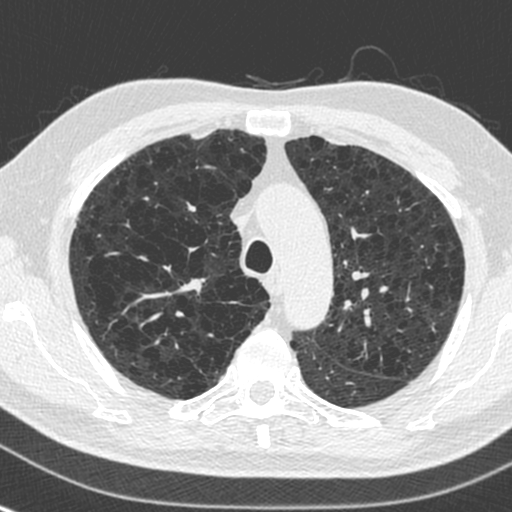
Axial slice from a low-dose chest CT screening exam; baseline annual screen; lung window (W 1500 / L -600 HU); standard (soft-tissue) reconstruction kernel (C). Male participant, aged 73 years at enrolment. Current smoker at enrolment.
Lesion marked by an expert reader, bounding box [x1, y1, x2, y2] px = [149, 248, 196, 286]. Screening reader's record for this exam: no non-calcified nodule ≥4 mm recorded. Official screen result: negative screen, significant abnormalities not suspicious for lung cancer.